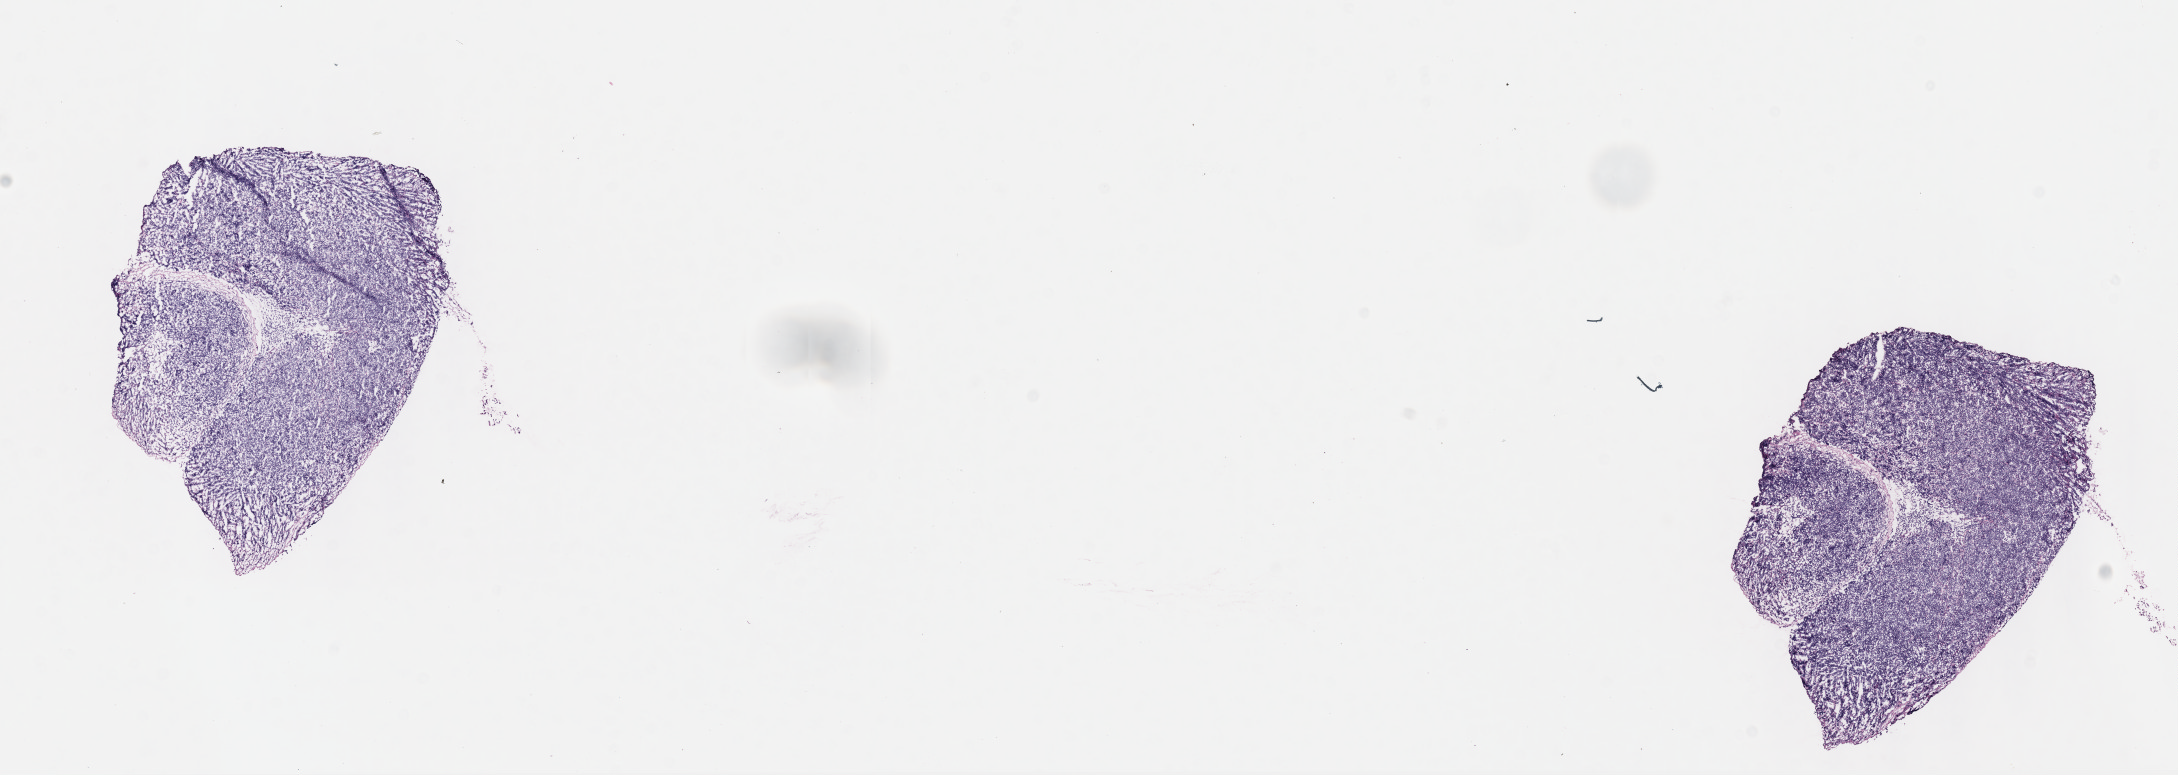
Digitized H&E-stained section — shown as a low-resolution overview of the whole scanned area (about 17.6 x 6.3 mm); frozen section; primary tumor; anatomic site: mandible. Male patient; age at initial diagnosis 6 years. Slide review estimates, as recorded: tumor cells 90%, tumor nuclei 90%, stromal cells 10%, necrosis 0%, normal cells 0%. Infiltration values recorded for this section: lymphocyte infiltration 10%, monocyte infiltration 10%, neutrophil infiltration 0%.
* histologic diagnosis: Burkitt lymphoma, NOS
* section: top of the tissue portion
* Ann Arbor stage (patient): Stage IV